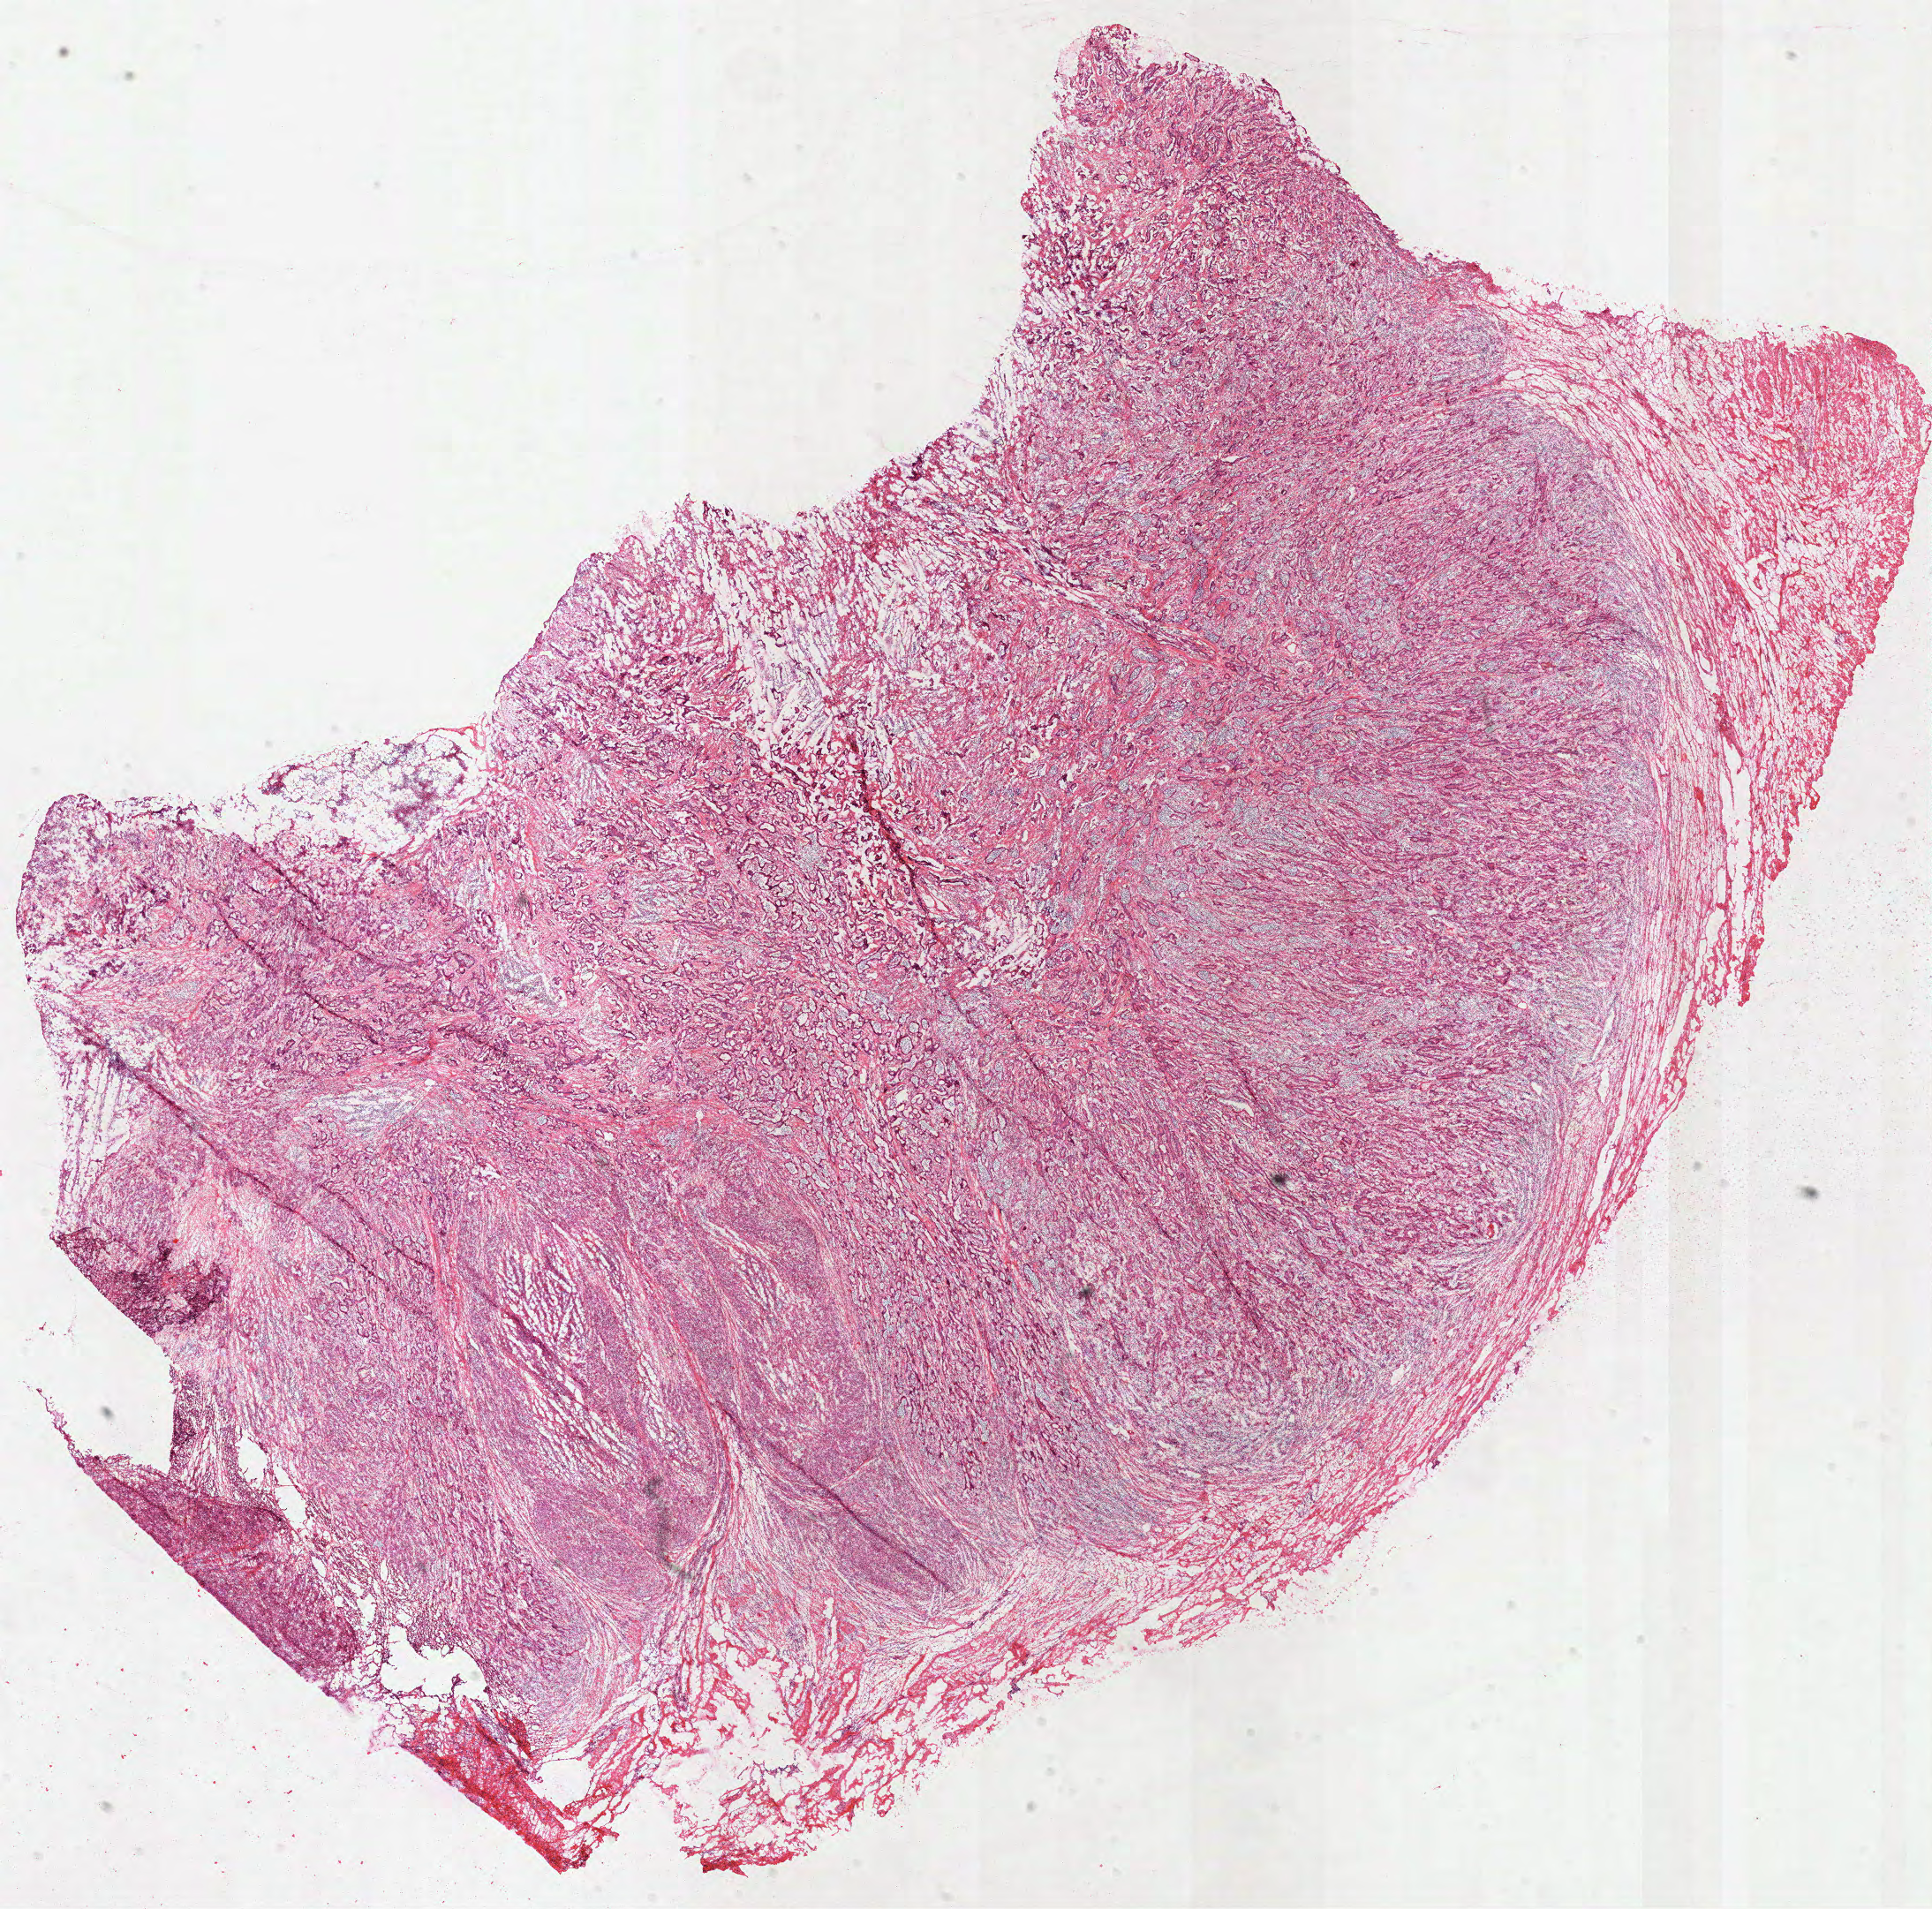
H&E whole-slide image, low-resolution overview of the scanned area, about 17.6 x 17.4 mm; frozen section from the top of the tissue portion; stomach, primary tumour sample. Female, age 67 years at initial diagnosis. Slide review estimates, as recorded: tumour cells 90%, tumour nuclei 61%.
Histologic diagnosis: Adenocarcinoma, NOS (gastric antrum).